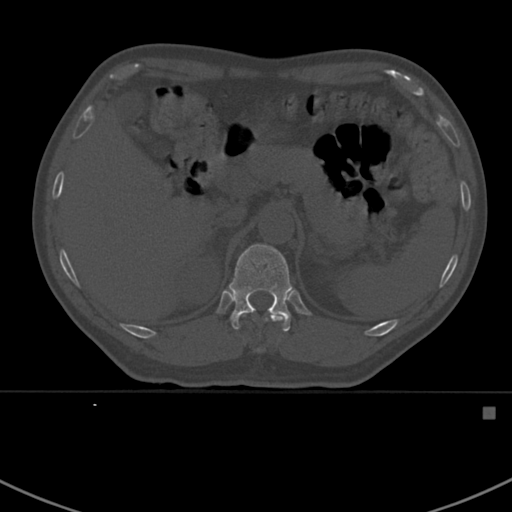
CT including the spine, one axial slice; slice 335 of 412 in the series (ordered by position); reconstruction kernel Br40s; 120 kVp; bone window (W 1800 / L 400 HU); 1.5 mm slice thickness; 512 × 512 image matrix, field of view 358 × 358 mm. Male patient, age 59 years. Case-level facts recorded for this patient, not image findings: primary cancer: prostate.
Annotated regions visible in this slice (semi-automatic segmentation, software-assisted and operator-edited):
- T11 vertebra: bounding box [x1, y1, x2, y2] px = [266, 315, 283, 322]
- T12 vertebra: [229, 244, 293, 332]